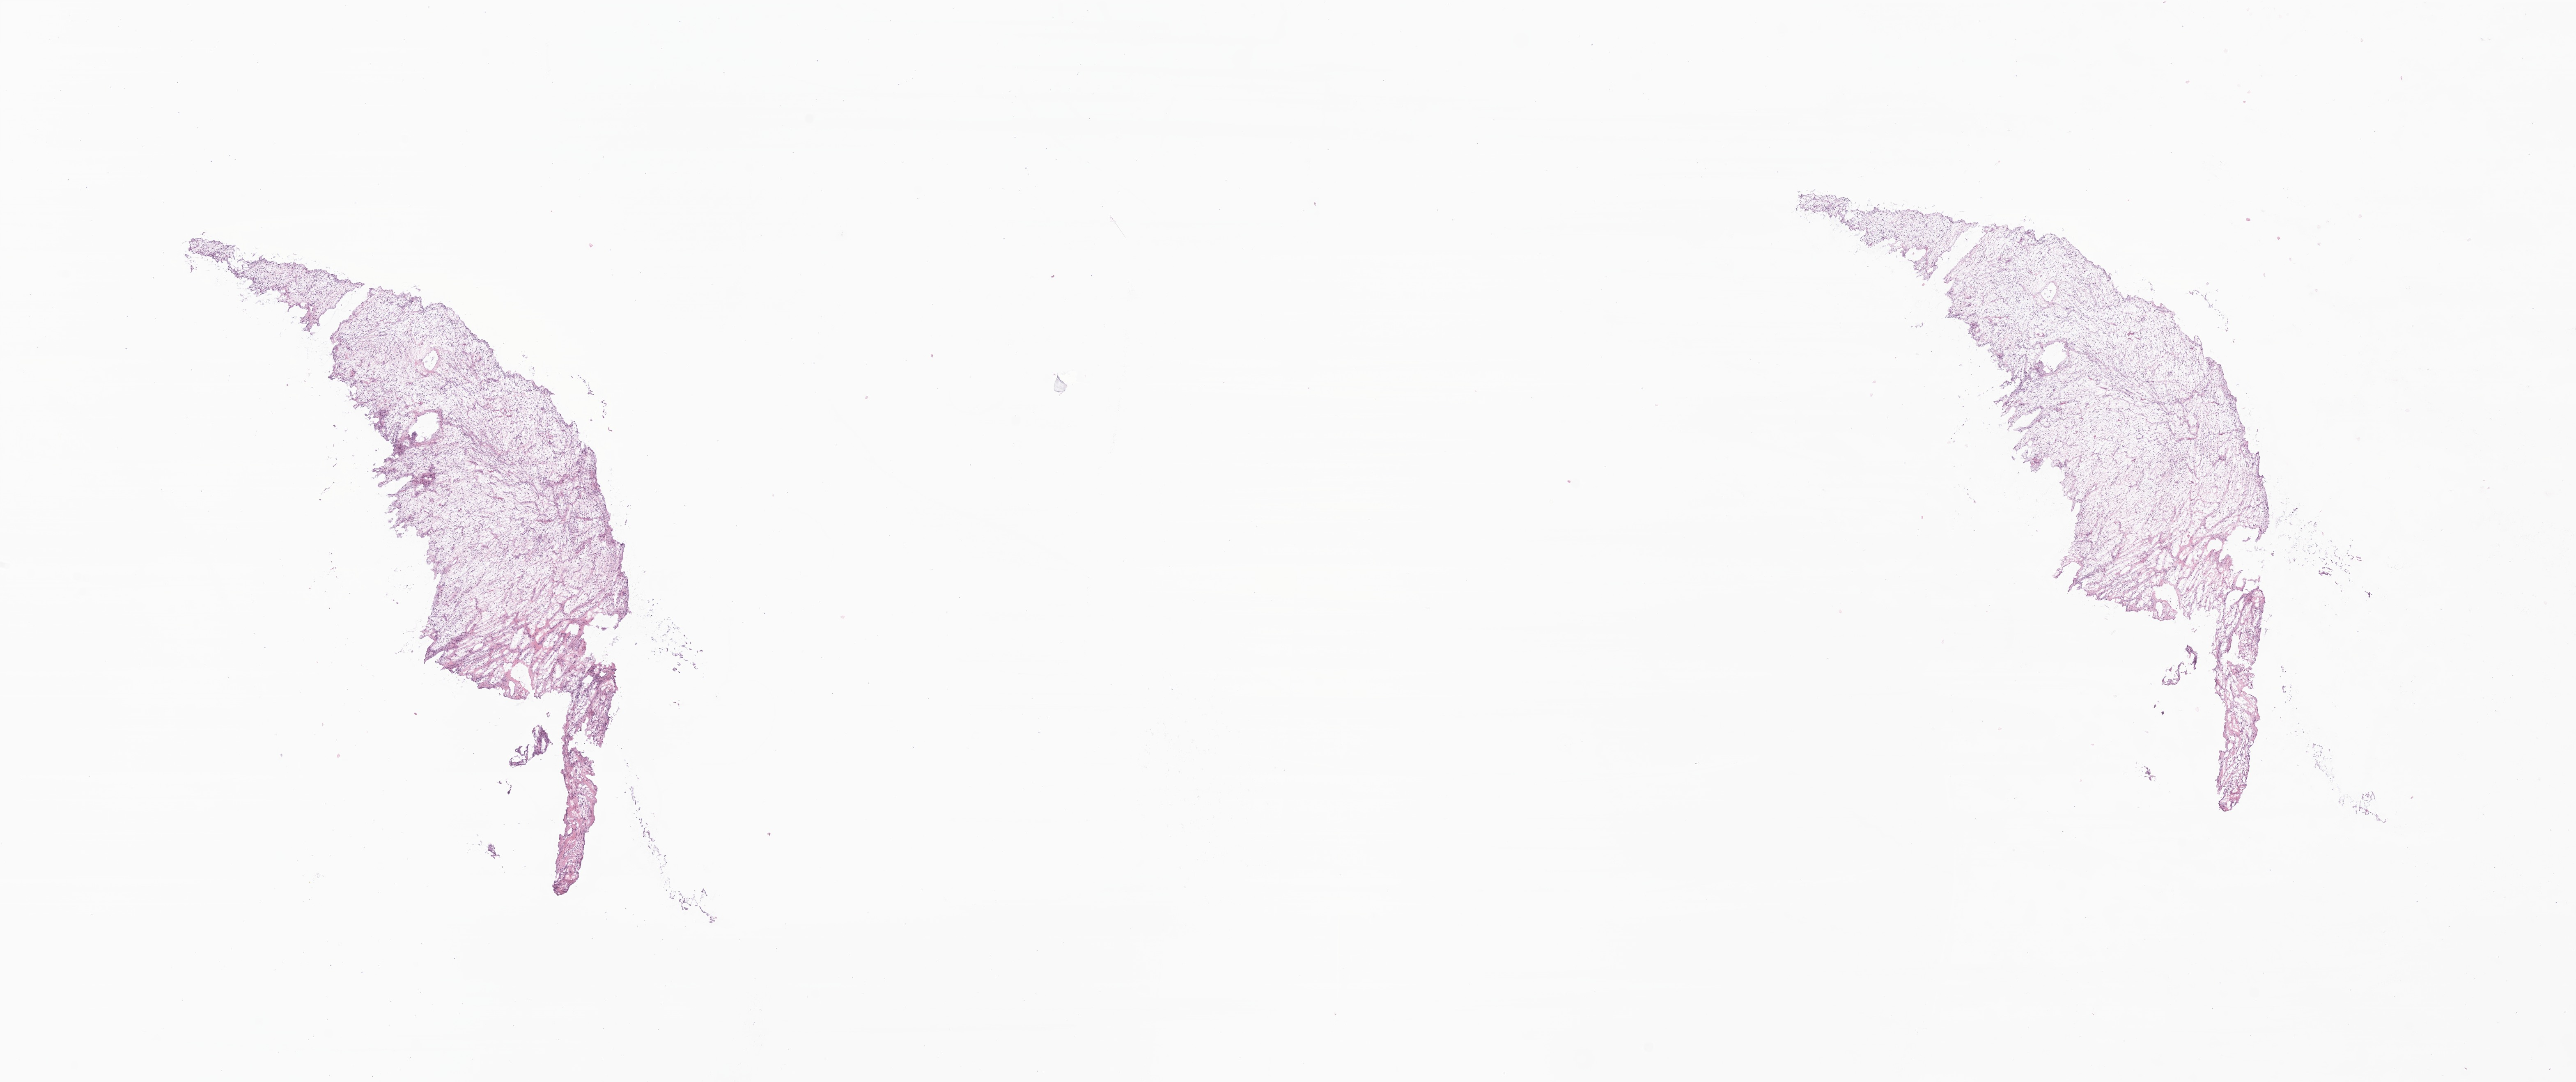
Haematoxylin and eosin whole-slide image of tumor tissue from the testis, whole scanned area (about 26.4 x 11.1 mm) shown as a low-resolution overview; frozen section. Patient male; age 187 months.
- recorded diagnosis: Rhabdomyosarcoma, NOS